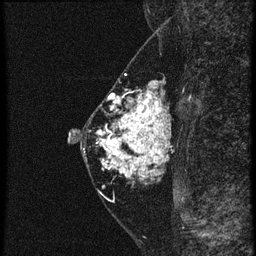
Breast MRI (dynamic contrast-enhanced), one sagittal slice. Slice 25 of 60 in the series (ordered by position). 4 images stored at this slice position (order not interpretable as contrast timing). 1.5 T. TE 4.2 ms, TR 20.4 ms. 1.5 mm slice thickness. 256 × 256 image matrix, field of view 180 × 180 mm. Female patient, age 46 years. Case-level facts recorded for this patient, not image findings: setting: breast cancer imaged before/during neoadjuvant chemotherapy; receptor status: triple-negative.
Annotated regions visible in this slice (semi-automatic segmentation, software-assisted and operator-edited):
- analysis volume of interest (the breast-tissue region the enhancement analysis was run in; not a lesion): bounding box (x1, y1, x2, y2) in pixels: (88, 82, 169, 185)
- tumour enhancement mask (voxels above the 90 % enhancement threshold inside the analysis volume of interest): (98, 82, 169, 177)